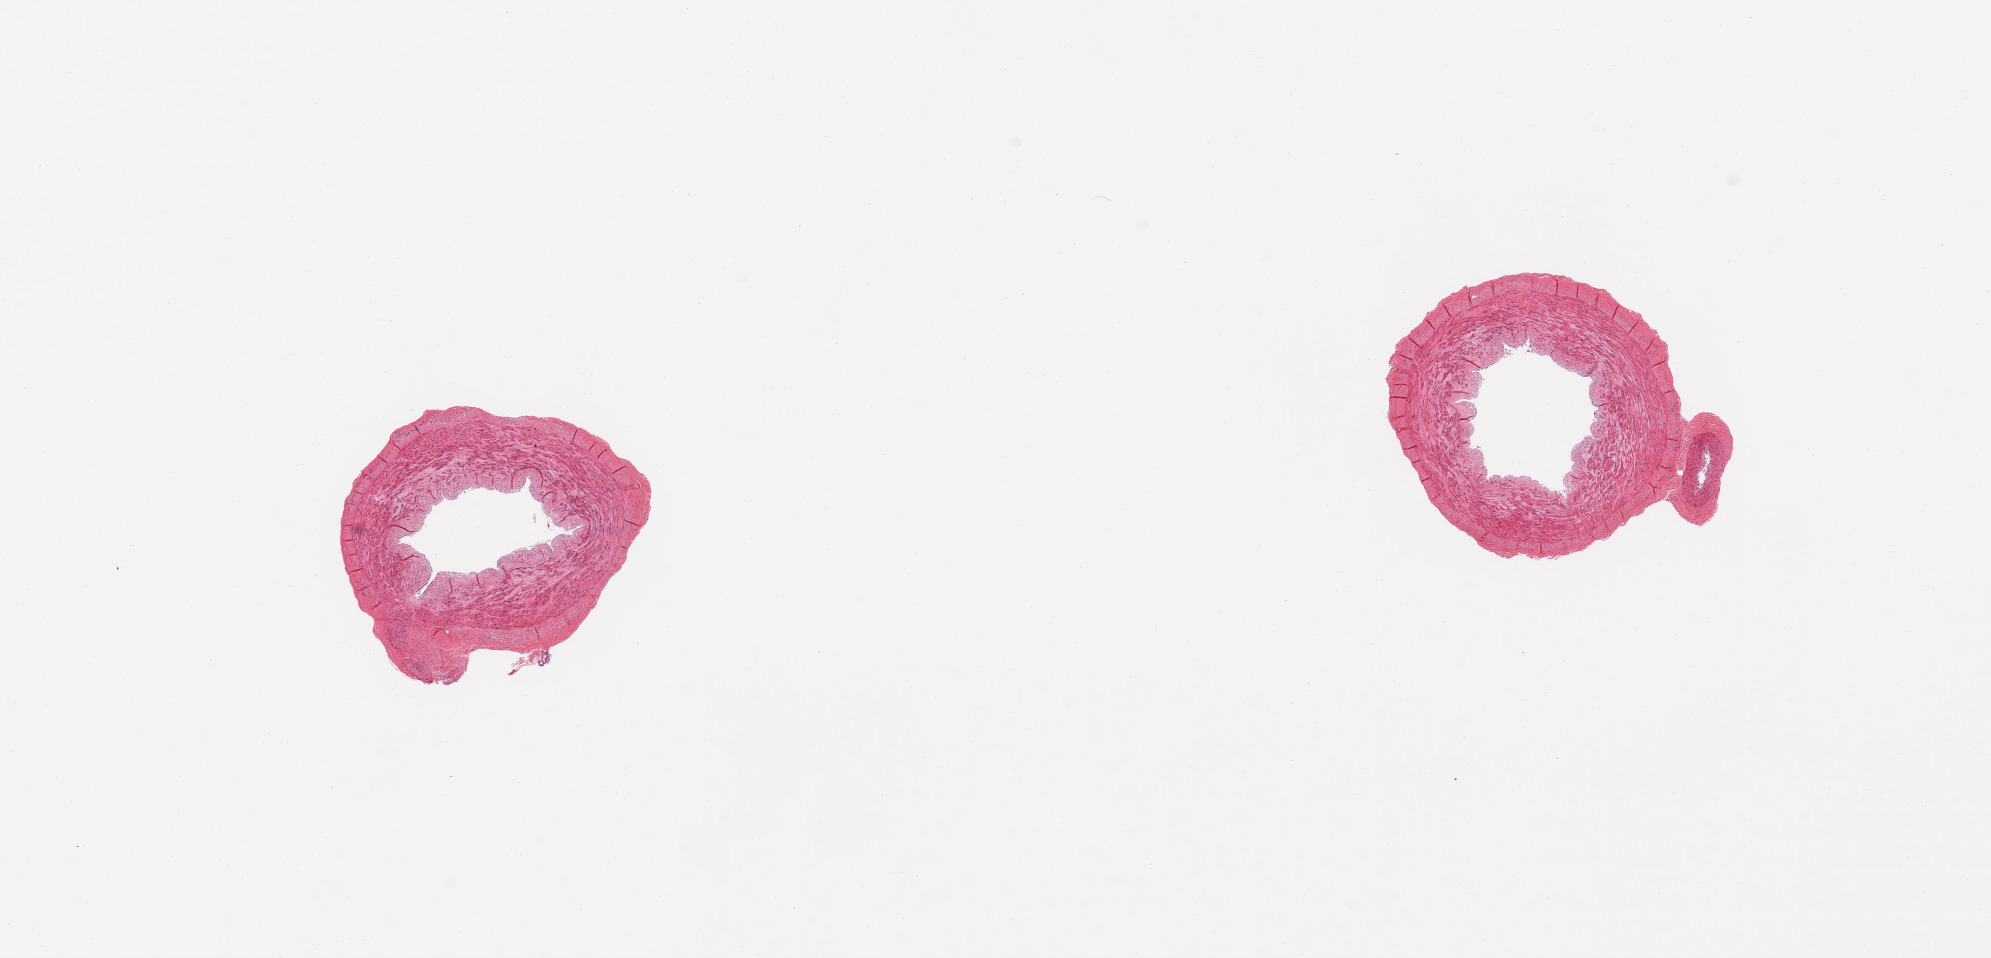
Digitized hematoxylin and eosin (H&E)-stained section, brightfield, whole scanned area (about 15.8 x 7.6 mm) shown as a low-resolution overview, PAXgene-fixed, paraffin-embedded tissue, section of tibial artery (target tissue), donor tissue sample. Donor sex: male.
Pathologist's review note for this sample: 2 pieces; well trimmed.